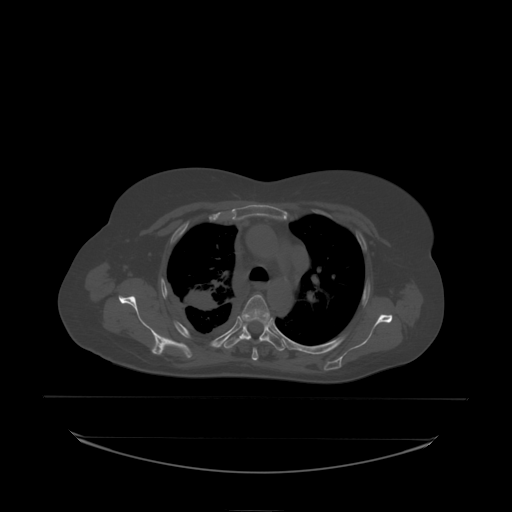
CT including the spine, one axial slice. Position 162 of 242 along the scan axis. Bone window (W 1800 / L 400 HU). 2.5 mm slice thickness. 512 × 512 image matrix, field of view 500 × 500 mm. Female patient, age 53 years. From the clinical record (not read from this slice): primary cancer: lung; vertebrae with lytic lesions (as recorded): T7, L1.
Outlined on this slice (semi-automatic segmentation, software-assisted and operator-edited):
- T4 vertebra: bounding box <242,295,271,322> (left, top, right, bottom; pixels)
- T5 vertebra: <238,319,276,338>